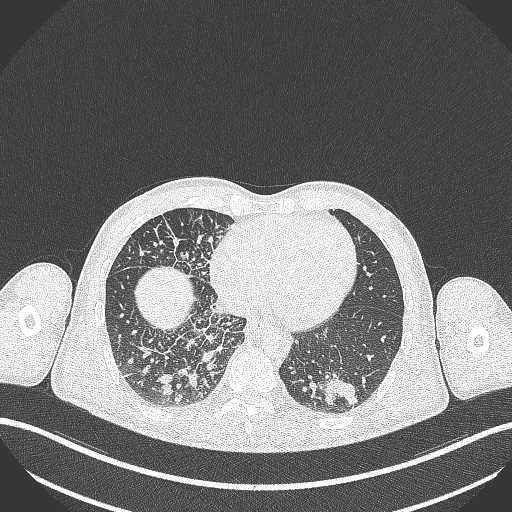
Chest CT, one axial slice; slice 96 of 348 in the series (ordered by position); reconstruction kernel B70f; 120 kVp; lung window (W 1500 / L -600 HU); 1 mm slice thickness; 512 × 512 image matrix. Male patient, age 49 years. From the clinical record (not read from this slice): clinical TNM (as recorded): T2b N1 M0.
Structures marked on this image (rectangle marked by the reading radiologist):
- lung tumour (recorded histology: adenocarcinoma): bounding box <322,367,363,411> (left, top, right, bottom; pixels)